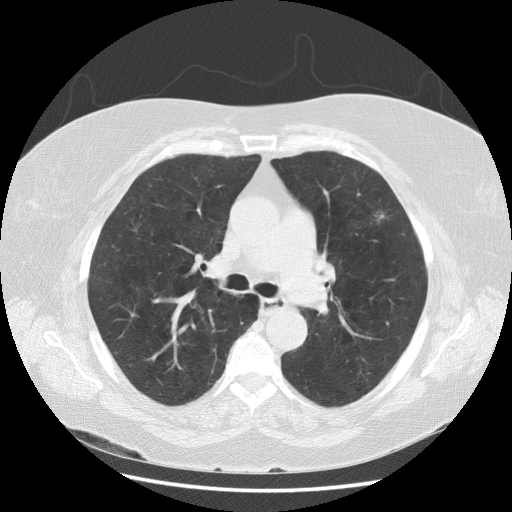
Chest CT (low-dose screening protocol), one axial image, second screening round (one year after baseline), lung window (W 1500 / L -600 HU), 2.5 mm slice thickness, standard (soft-tissue) reconstruction kernel (STANDARD), 120 kVp, slice 62 of 164 in the series, 512 × 512 image matrix, field of view 380 × 380 mm. Female participant, aged 68 years at enrolment. Current smoker at enrolment.
• Lesion marked by an expert reader, bounding box [x1, y1, x2, y2] px = [362, 205, 395, 231].
• The screening reader recorded 2 non-calcified nodules or masses ≥4 mm on this exam (left upper lobe, right upper lobe); which of them this box marks is not recorded.
• Lung cancer was diagnosed 90 days after this screen: large cell carcinoma, NOS, left upper lobe, undifferentiated (G4), stage IA (AJCC 6th edition), 10 mm at pathology.